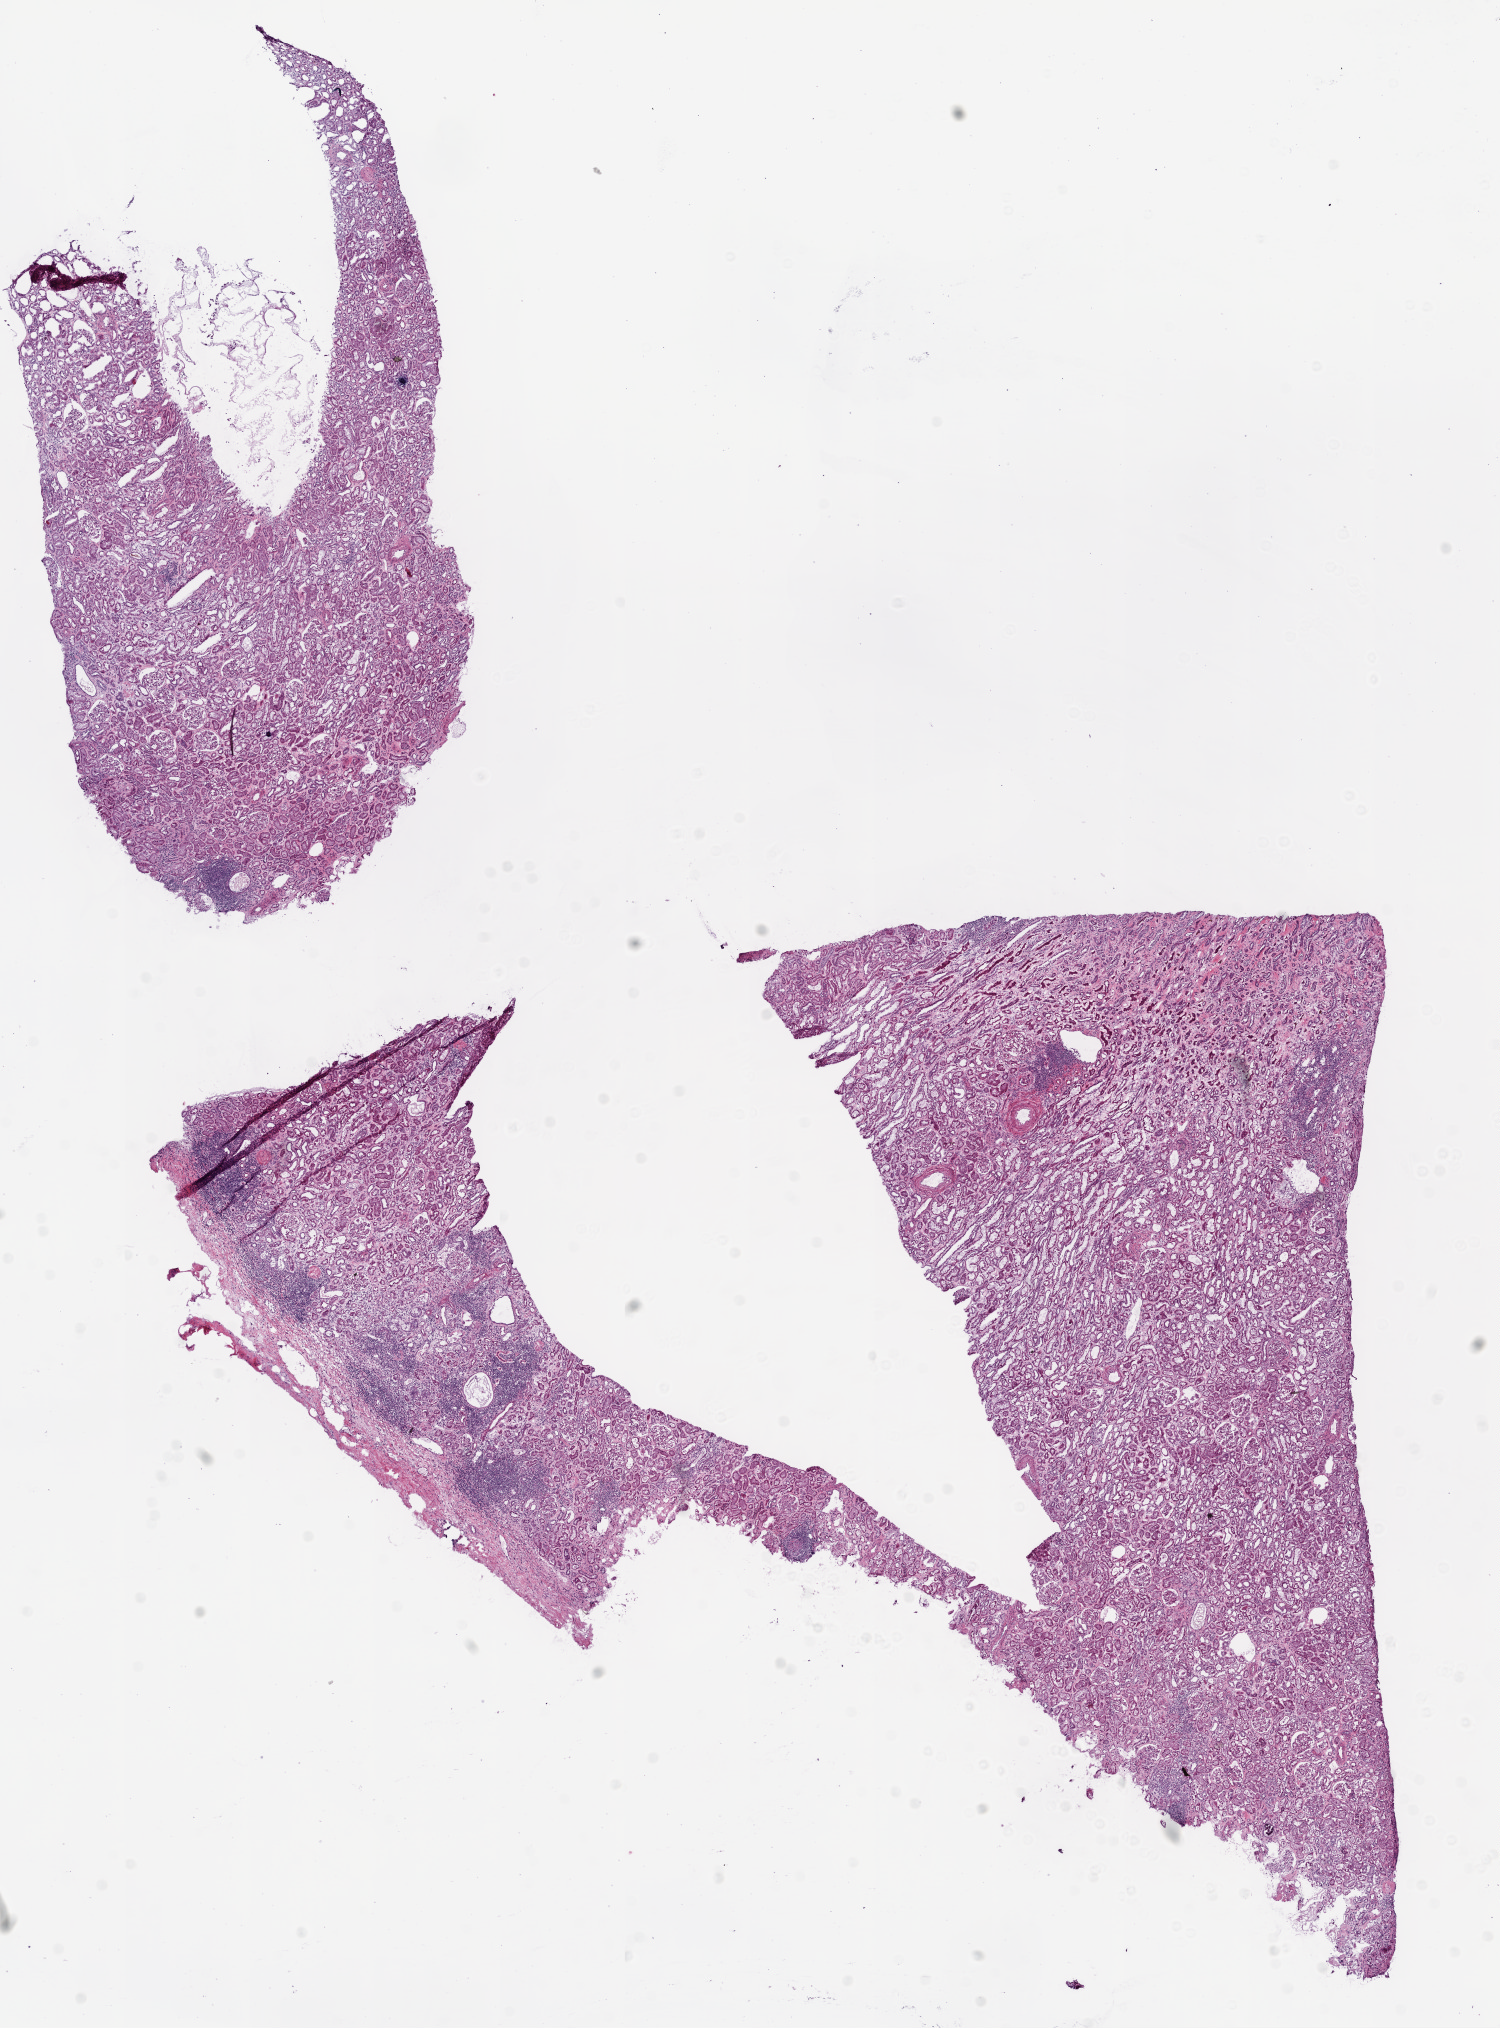
Whole-slide histology image, Hematoxylin and eosin (H&E) stained, low-resolution overview of the scanned area, about 12.0 x 16.3 mm (acquisition: 20x scan); frozen section from the bottom of the tissue portion; sample: solid tissue normal (non-tumour tissue), kidney. Male patient; age at initial diagnosis 64 years.
• this section: solid tissue normal (non-tumour) sample from the same patient
• patient diagnosis: Clear cell adenocarcinoma, NOS